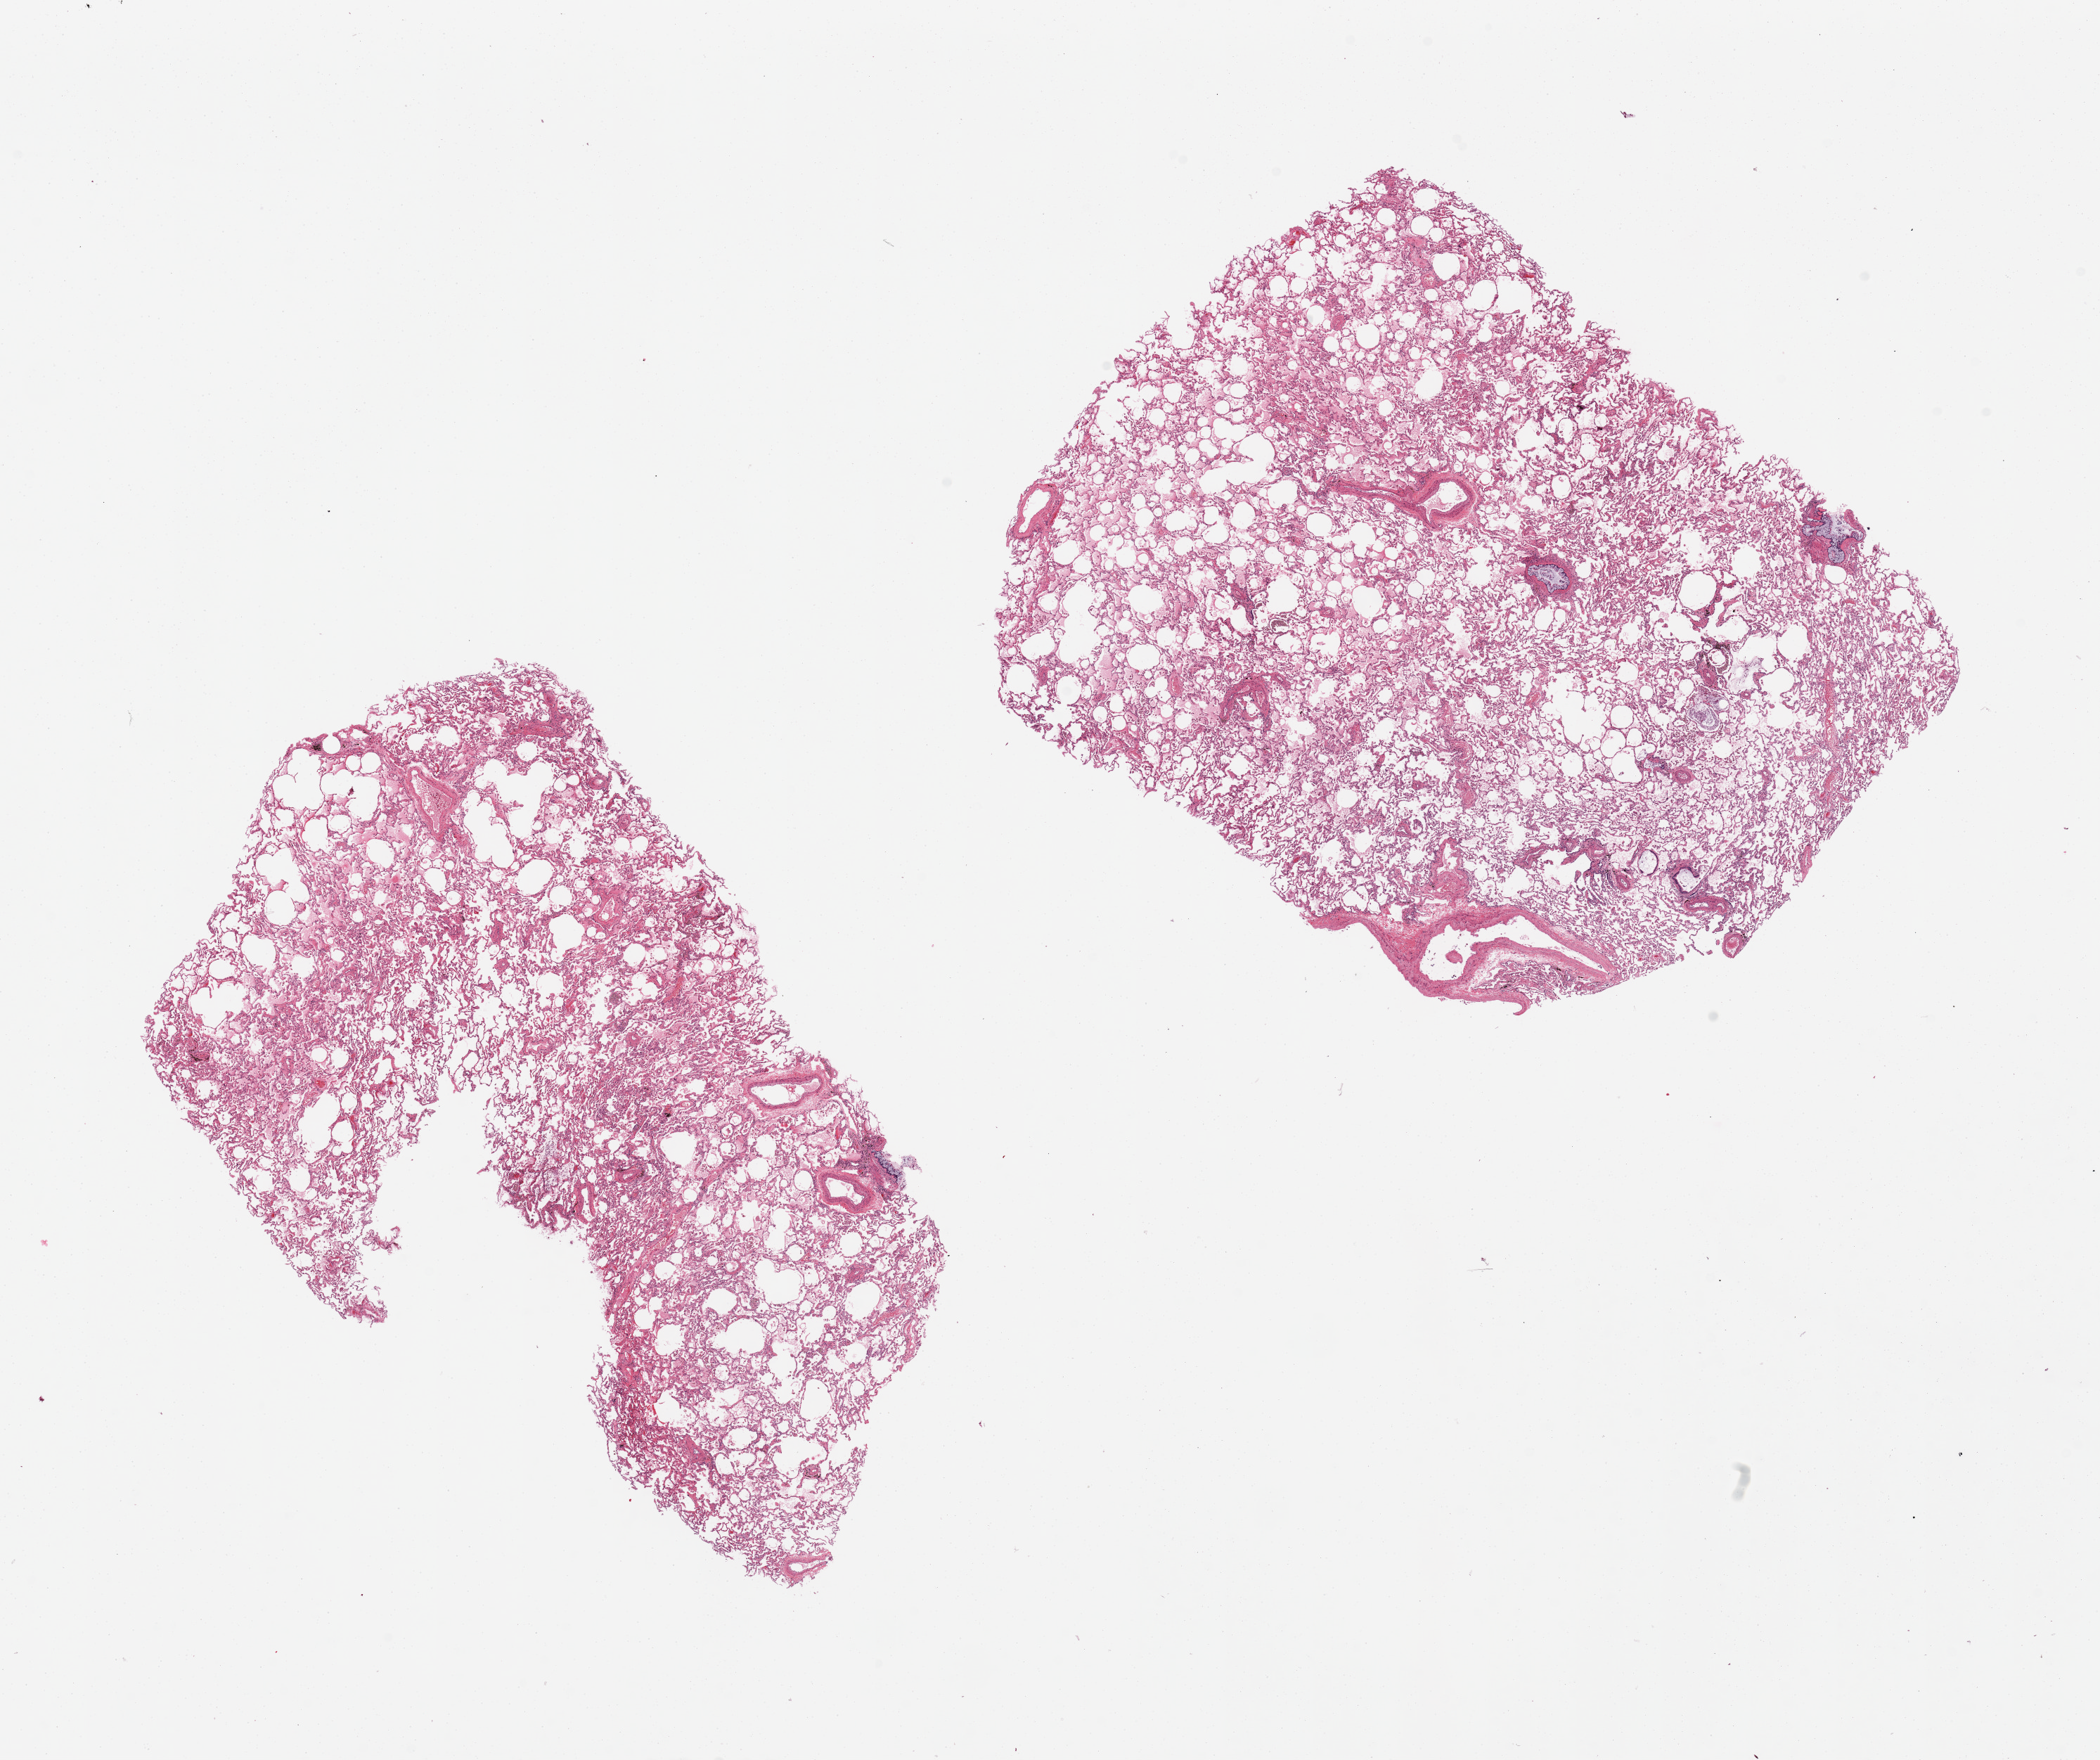
Whole-slide image, hematoxylin and eosin (H&E) stain — low-resolution overview of the scanned area, about 23.6 x 19.8 mm (acquisition: 20x scan). PAXgene-fixed paraffin-embedded (PFPE) section. Target tissue: lung. Donor tissue sample.
* review note (as recorded): 2 pieces, numerous hemosiderin-laden macrophages, increased goblet cells and thickening of the basement membrane c/w history of asthma